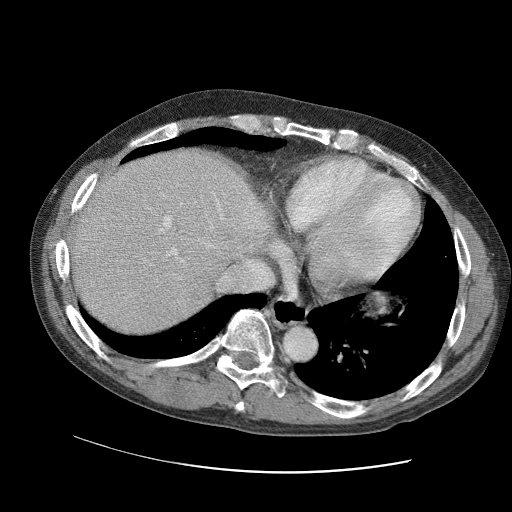
Contrast-enhanced abdominal CT (liver protocol), one axial slice. Position 85 of 109 along the scan axis. 120 kVp. Soft-tissue window (W 400 / L 40 HU). 2.5 mm slice thickness. 512 × 512 image matrix. Case-level facts recorded for this patient, not image findings: diagnosis: hepatocellular carcinoma (patient treated with transarterial chemoembolisation; whether this scan precedes or follows treatment is not stated here); TNM stage (as recorded): Stage-IIIC; Child-Pugh class: B; tumour differentiation: well differentiated.
Outlined on this slice (semi-automatically segmented with operator editing):
- liver parenchyma outside the tumour (the mass and vessels are separate outlines, so this box may not span the whole liver): bounding box <66,148,272,334> (left, top, right, bottom; pixels)
- liver vessels: <148,193,254,266>